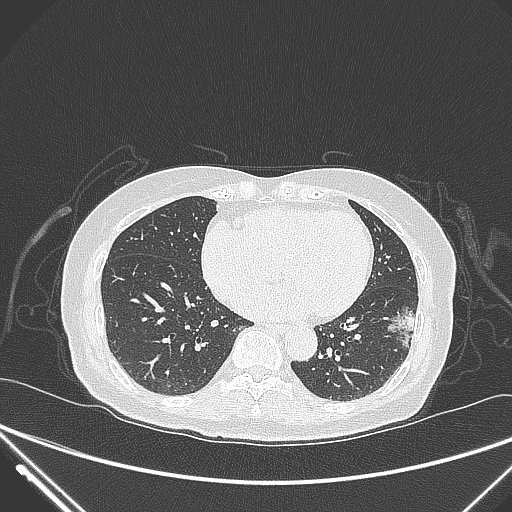
Chest CT, one axial slice. 120 kVp. Lung window (W 1500 / L -600 HU). 1 mm slice thickness. 512 × 512 image matrix, field of view 377 × 377 mm. Female patient, age 82 years. From the clinical record (not read from this slice): clinical TNM (as recorded): T1c N0 M0.
Outlined on this slice (rectangle marked by the reading radiologist):
- lung tumour (recorded histology: adenocarcinoma): bounding box [x1, y1, x2, y2] px = [384, 302, 422, 354]